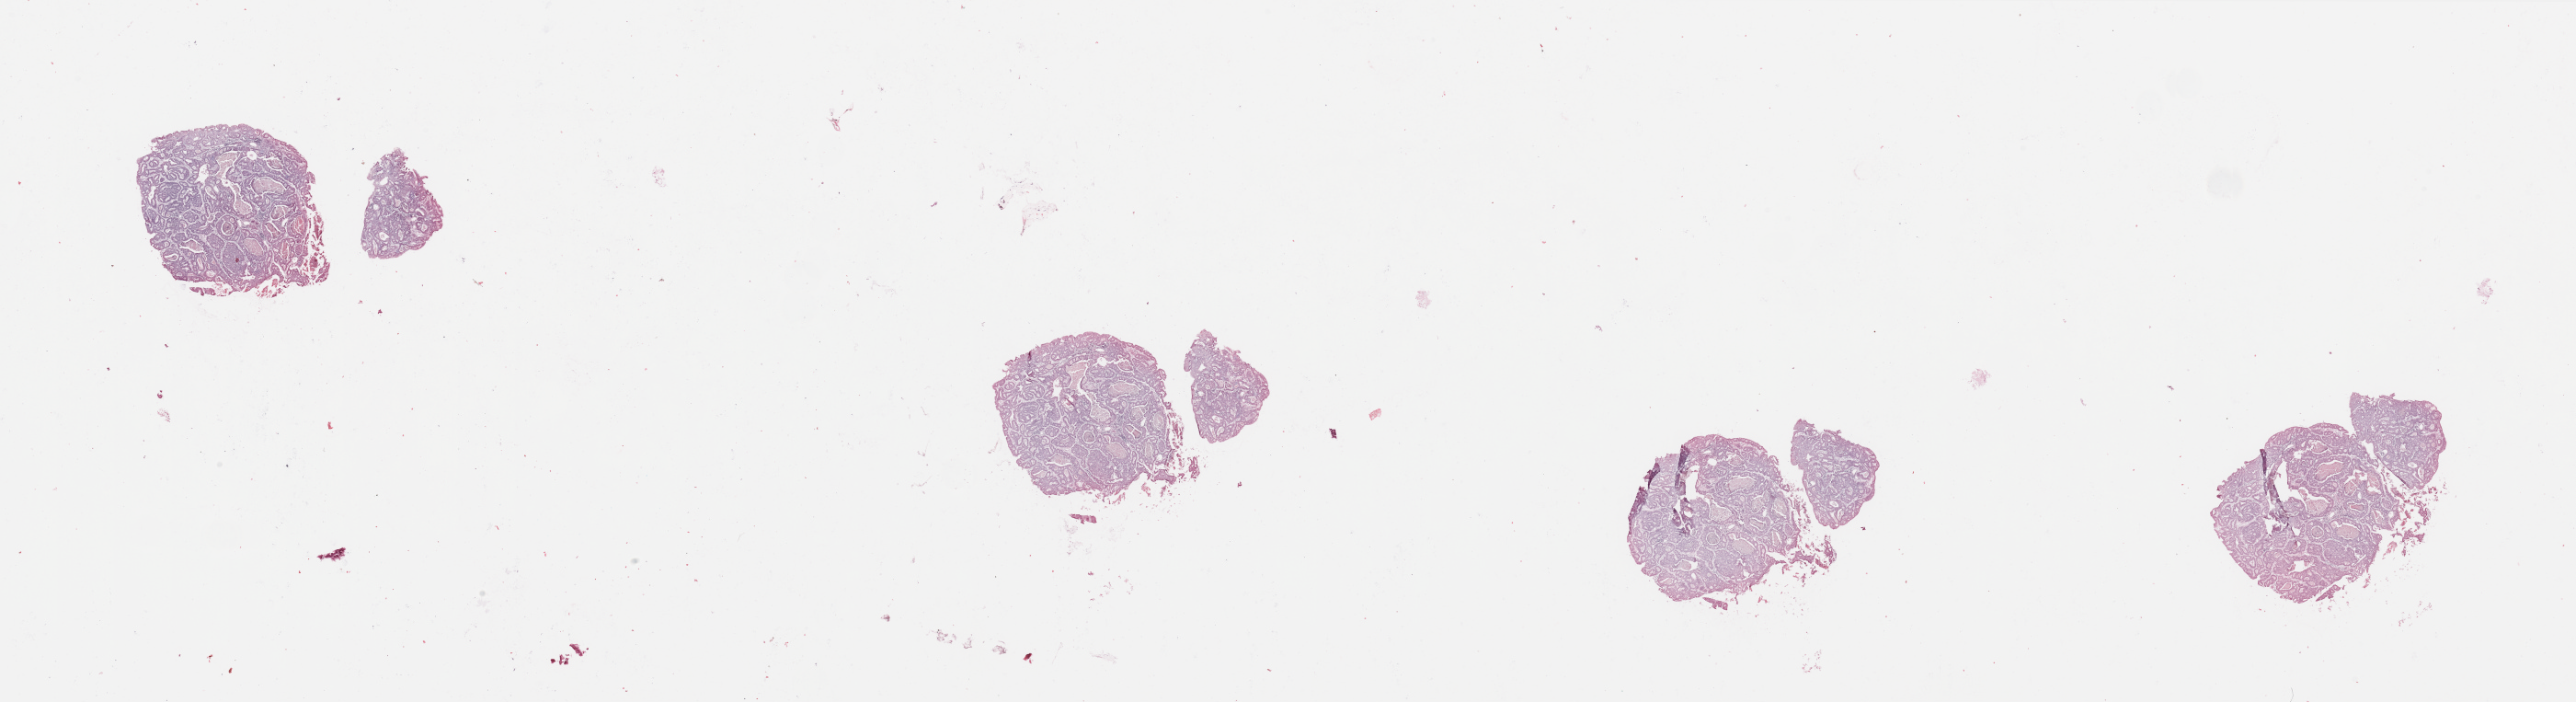
Whole-slide histology image, H&E-stained, shown as a low-resolution overview of the whole scanned area (about 44.3 x 12.1 mm, from a 20x scan). Uterus, tumour tissue. 65-year-old female patient. Histologic grade: G2 (moderately differentiated).
- AJCC pathologic stage: III
- diagnosis: Endometrioid adenocarcinoma, NOS
- primary tumour site (as recorded): anterior endometrium